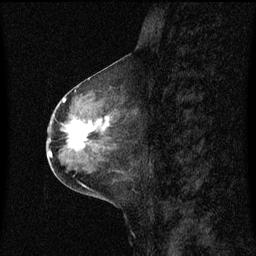
Breast MRI (dynamic contrast-enhanced), one sagittal slice. Slice 29 of 60 in the series (ordered by position). Dynamic contrast-enhanced series, image 2 of 3 at this slice position (ordered by acquisition). 1.5 T. TE 4.2 ms, TR 8.4 ms. 2 mm slice thickness. 256 × 256 image matrix. Female patient, age 49 years. From the clinical record (not read from this slice): setting: breast cancer imaged before/during neoadjuvant chemotherapy; receptor status: HR-positive, HER2-negative.
Outlined on this slice (semi-automatic segmentation, software-assisted and operator-edited):
- analysis volume of interest (the breast-tissue region the enhancement analysis was run in; not a lesion): bounding box [x1, y1, x2, y2] px = [59, 101, 121, 158]
- tumour enhancement mask (voxels above the 70 % enhancement threshold inside the analysis volume of interest): [66, 116, 110, 150]